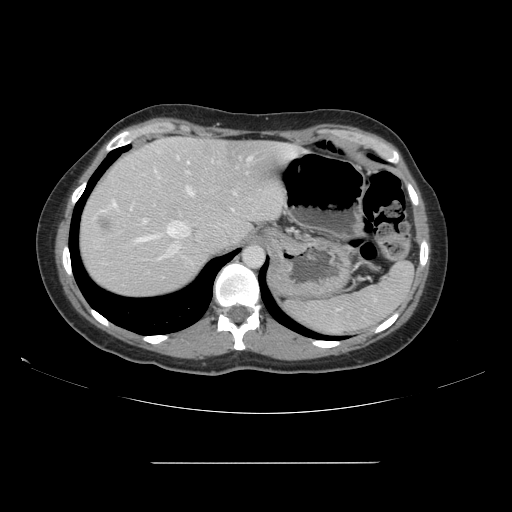
Contrast-enhanced abdominal CT, one axial slice. Intravenous contrast given. Soft-tissue window (W 400 / L 40 HU). 2.5 mm slice thickness. 512 × 512 image matrix. Female patient, age 46 years. Case-level facts recorded for this patient, not image findings: diagnosis: colorectal cancer liver metastases, imaged before liver resection; multiple liver metastases: yes; largest metastasis: 3 cm; disease in both lobes: yes.
Outlined on this slice (manually delineated by an expert):
- hepatic veins: box from (x=110, y=156) to (x=253, y=259) px
- liver: (x=80, y=138)–(x=295, y=297)
- planned liver remnant (the part of the liver to remain after resection): (x=93, y=138)–(x=296, y=248)
- portal vein (with intrahepatic branches): (x=231, y=192)–(x=236, y=212)
- liver metastasis: (x=97, y=217)–(x=113, y=232)